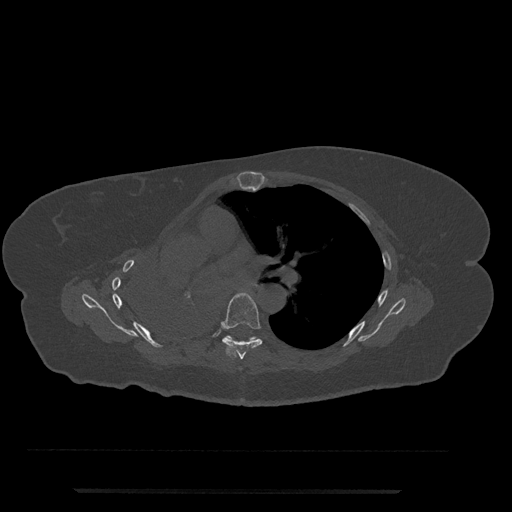
CT including the spine, one axial slice; slice 488 of 797 in the series (ordered by position); reconstruction kernel Br40s/3; 120 kVp; bone window (W 1800 / L 400 HU); 512 × 512 image matrix, field of view 440 × 440 mm. Patient: female, 51 years. From the clinical record (not read from this slice): primary cancer: neuro; vertebrae with lytic lesions (as recorded): T8.
Annotated regions visible in this slice (semi-automatic segmentation, software-assisted and operator-edited):
- T6 vertebra: bounding box (x1, y1, x2, y2) in pixels: (221, 292, 262, 360)
- T7 vertebra: (227, 335, 257, 341)